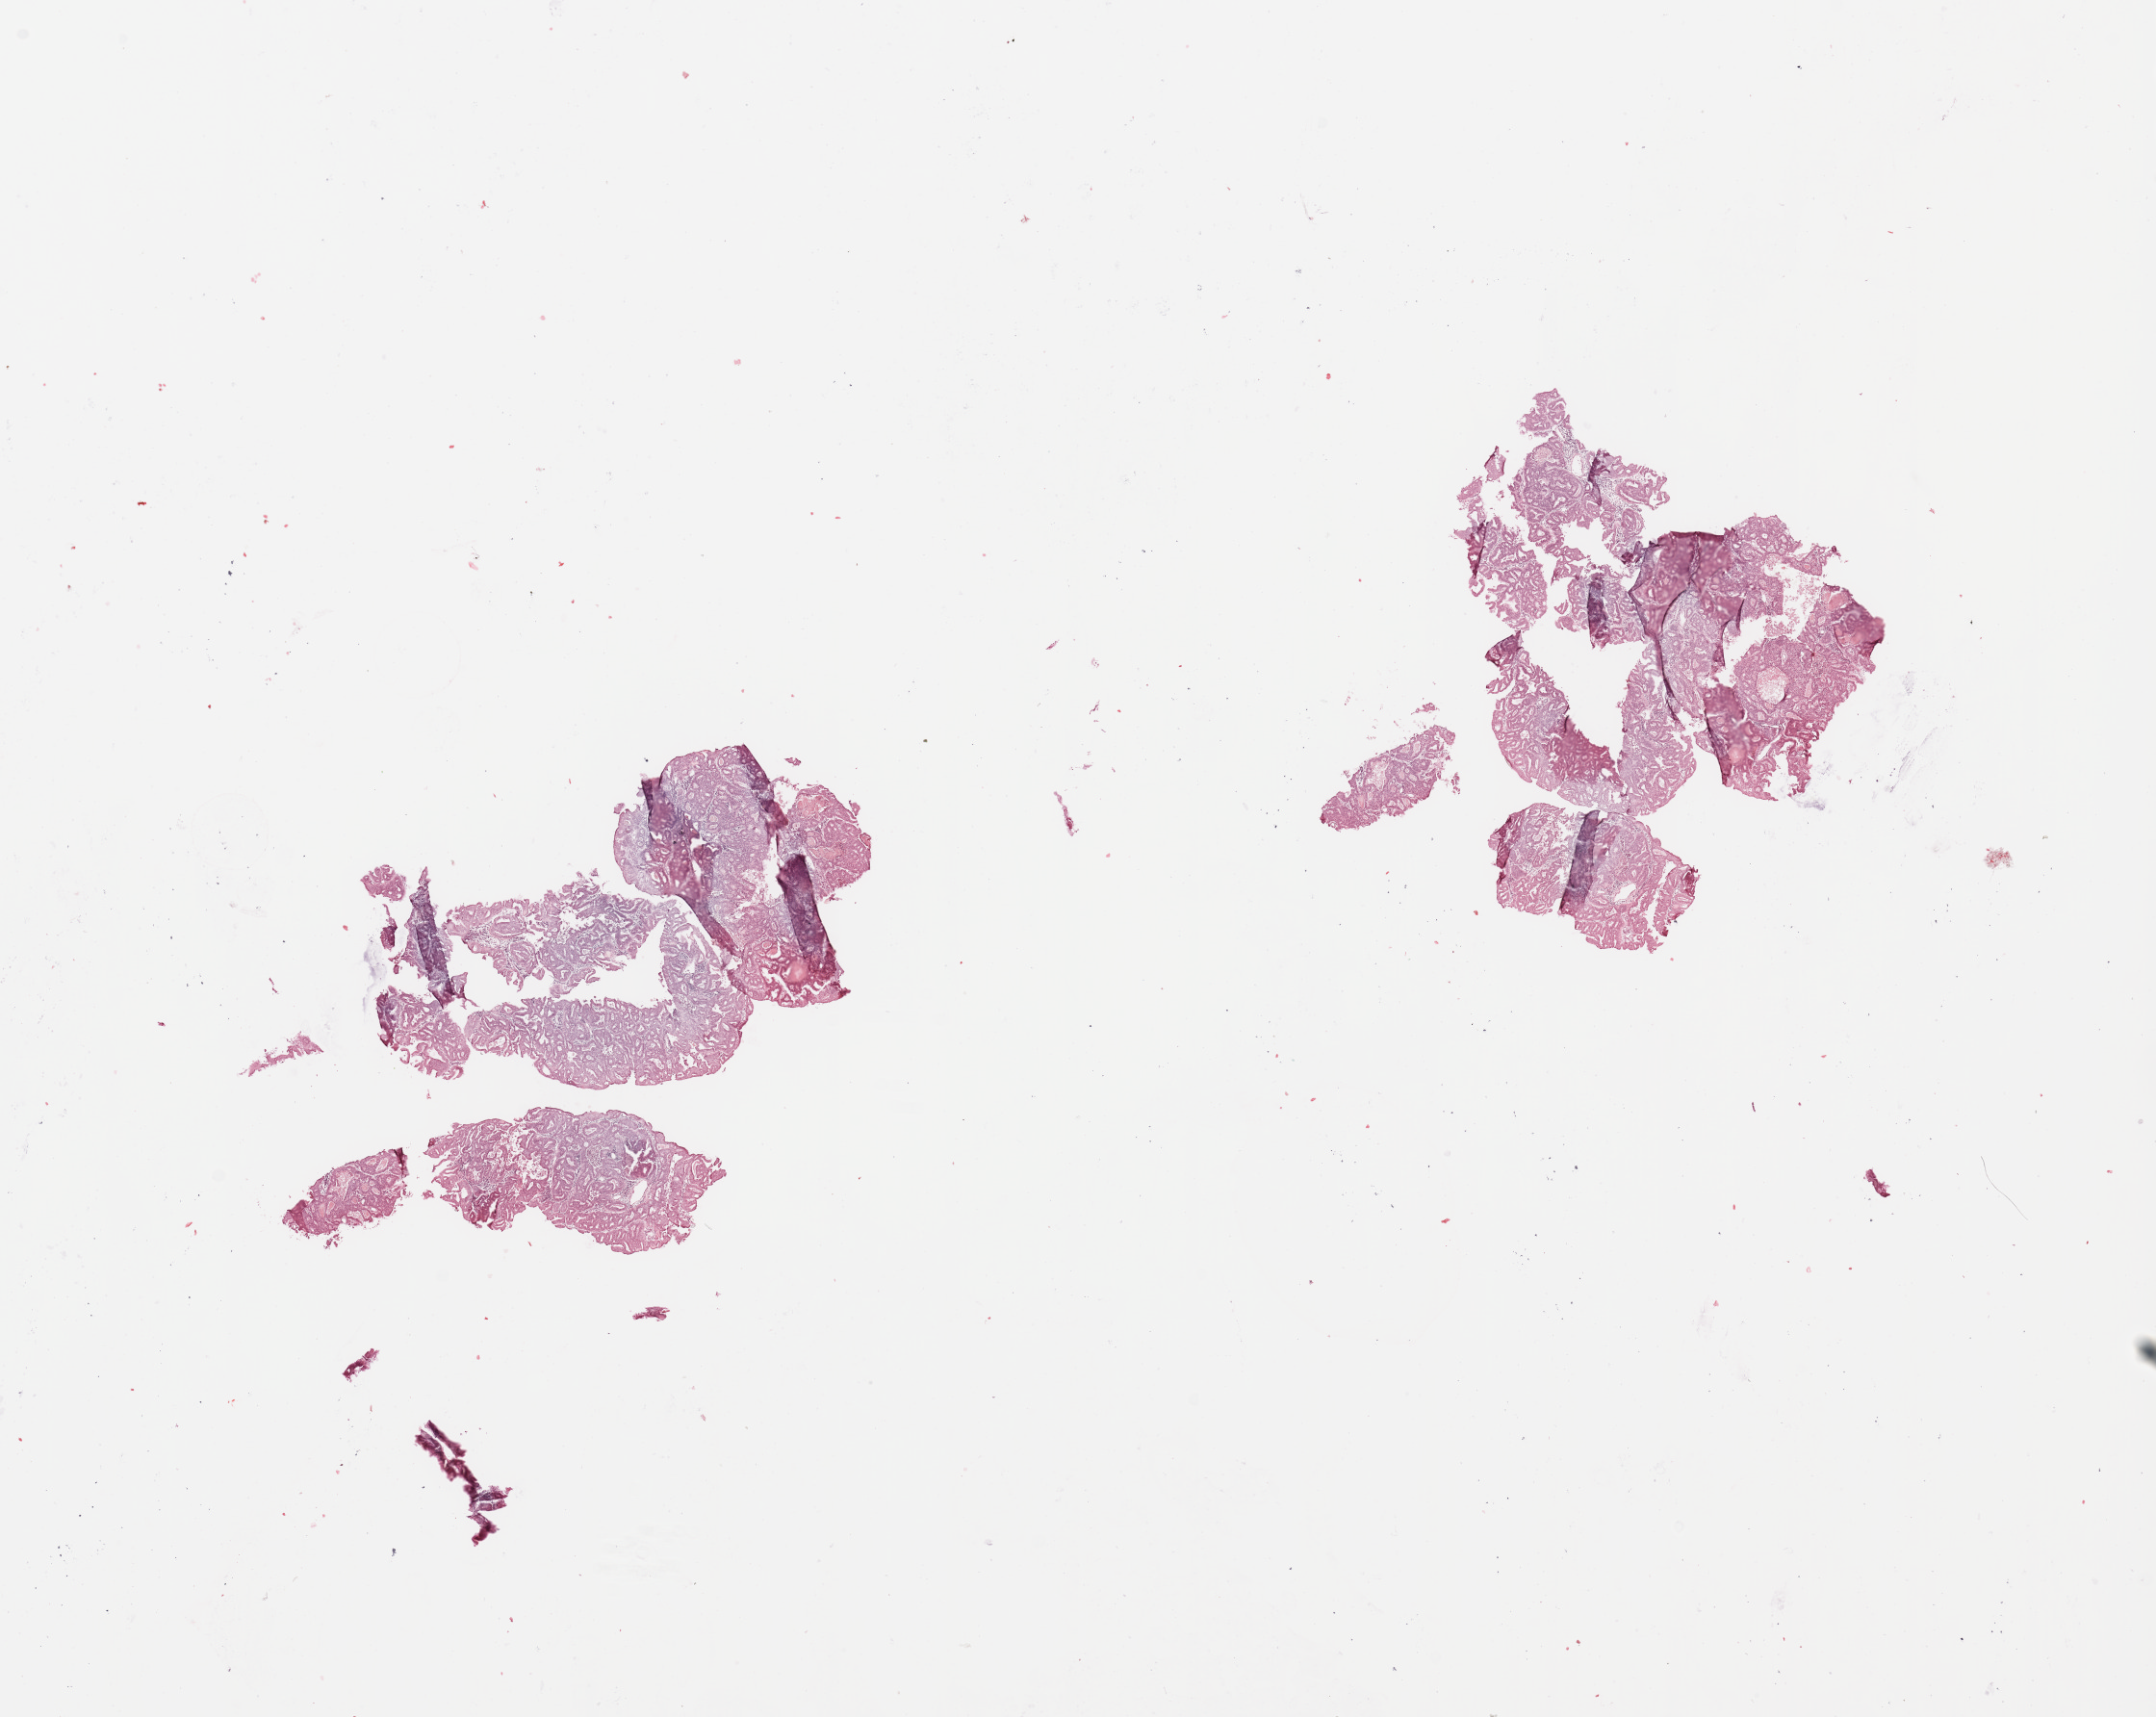
H&E-stained whole-slide image — a low-resolution overview of the entire scanned area, about 17.7 x 14.1 mm (slide scanned at 20x), tumour tissue sample, uterus. 65-year-old female patient. Histologic grade: G2 (moderately differentiated).
• diagnosis: Endometrioid adenocarcinoma, NOS
• AJCC pathologic stage: III
• primary tumour site (as recorded): anterior endometrium